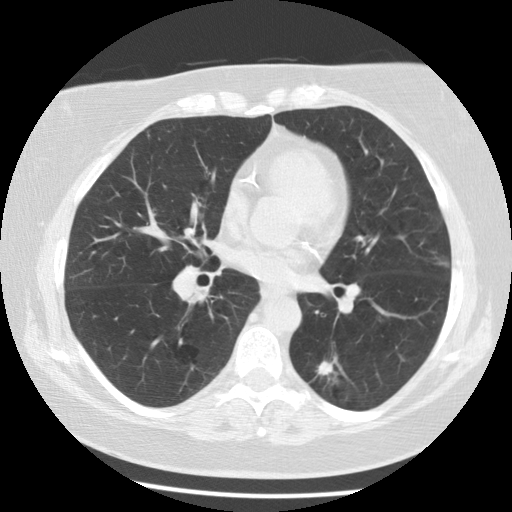
Low-dose screening chest CT, one axial slice; position 57 of 116 along the scan axis; 120 kVp; lung window (W 1500 / L -600 HU); 2.5 mm slice thickness; 512 × 512 image matrix, field of view 341 × 341 mm.
Outlined on this slice (outlined manually by an expert reader):
- lesion 1 (tumor, lower lobe of left lung): bounding box (x1, y1, x2, y2) in pixels: (317, 361, 334, 376)